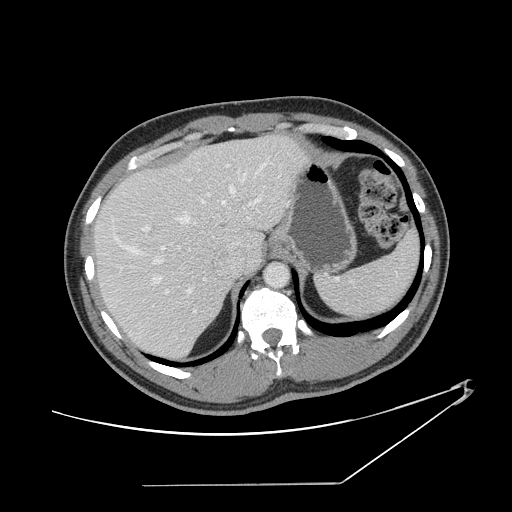
Contrast-enhanced abdominal CT, one axial slice; position 109 of 152 along the scan axis; reconstruction kernel STANDARD; 120 kVp; soft-tissue window (W 400 / L 40 HU); 2.5 mm slice thickness; 512 × 512 image matrix, field of view 432 × 432 mm. Male patient, age 45 years. Case-level facts recorded for this patient, not image findings: diagnosis: colorectal cancer liver metastases, imaged before liver resection; multiple liver metastases: no; largest metastasis: 1 cm; chemotherapy before resection: yes.
Structures marked on this image (expert manual segmentation):
- hepatic veins: bounding box (x1, y1, x2, y2) in pixels: (111, 157, 269, 295)
- liver: (95, 136, 301, 361)
- planned liver remnant (the part of the liver to remain after resection): (95, 156, 234, 361)
- portal vein (with intrahepatic branches): (161, 175, 280, 314)